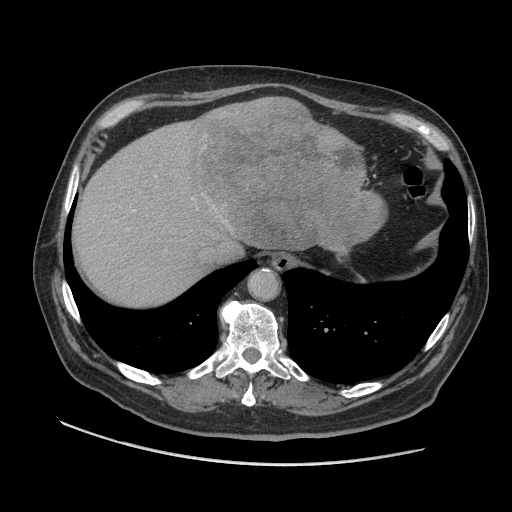
Contrast-enhanced abdominal CT (liver protocol), one axial slice; position 79 of 109 along the scan axis; soft-tissue window (W 400 / L 40 HU); 512 × 512 image matrix, field of view 420 × 420 mm. Case-level facts recorded for this patient, not image findings: diagnosis: hepatocellular carcinoma (patient treated with transarterial chemoembolisation; whether this scan precedes or follows treatment is not stated here); TNM stage (as recorded): Stage-I; Child-Pugh class: A.
Annotated regions visible in this slice (semi-automatic segmentation, software-assisted and operator-edited):
- abdominal aorta: bounding box (x1, y1, x2, y2) in pixels: (251, 272, 277, 298)
- liver parenchyma outside the tumour (the mass and vessels are separate outlines, so this box may not span the whole liver): (72, 96, 308, 306)
- mass: (189, 97, 387, 253)
- liver vessels: (133, 176, 194, 212)